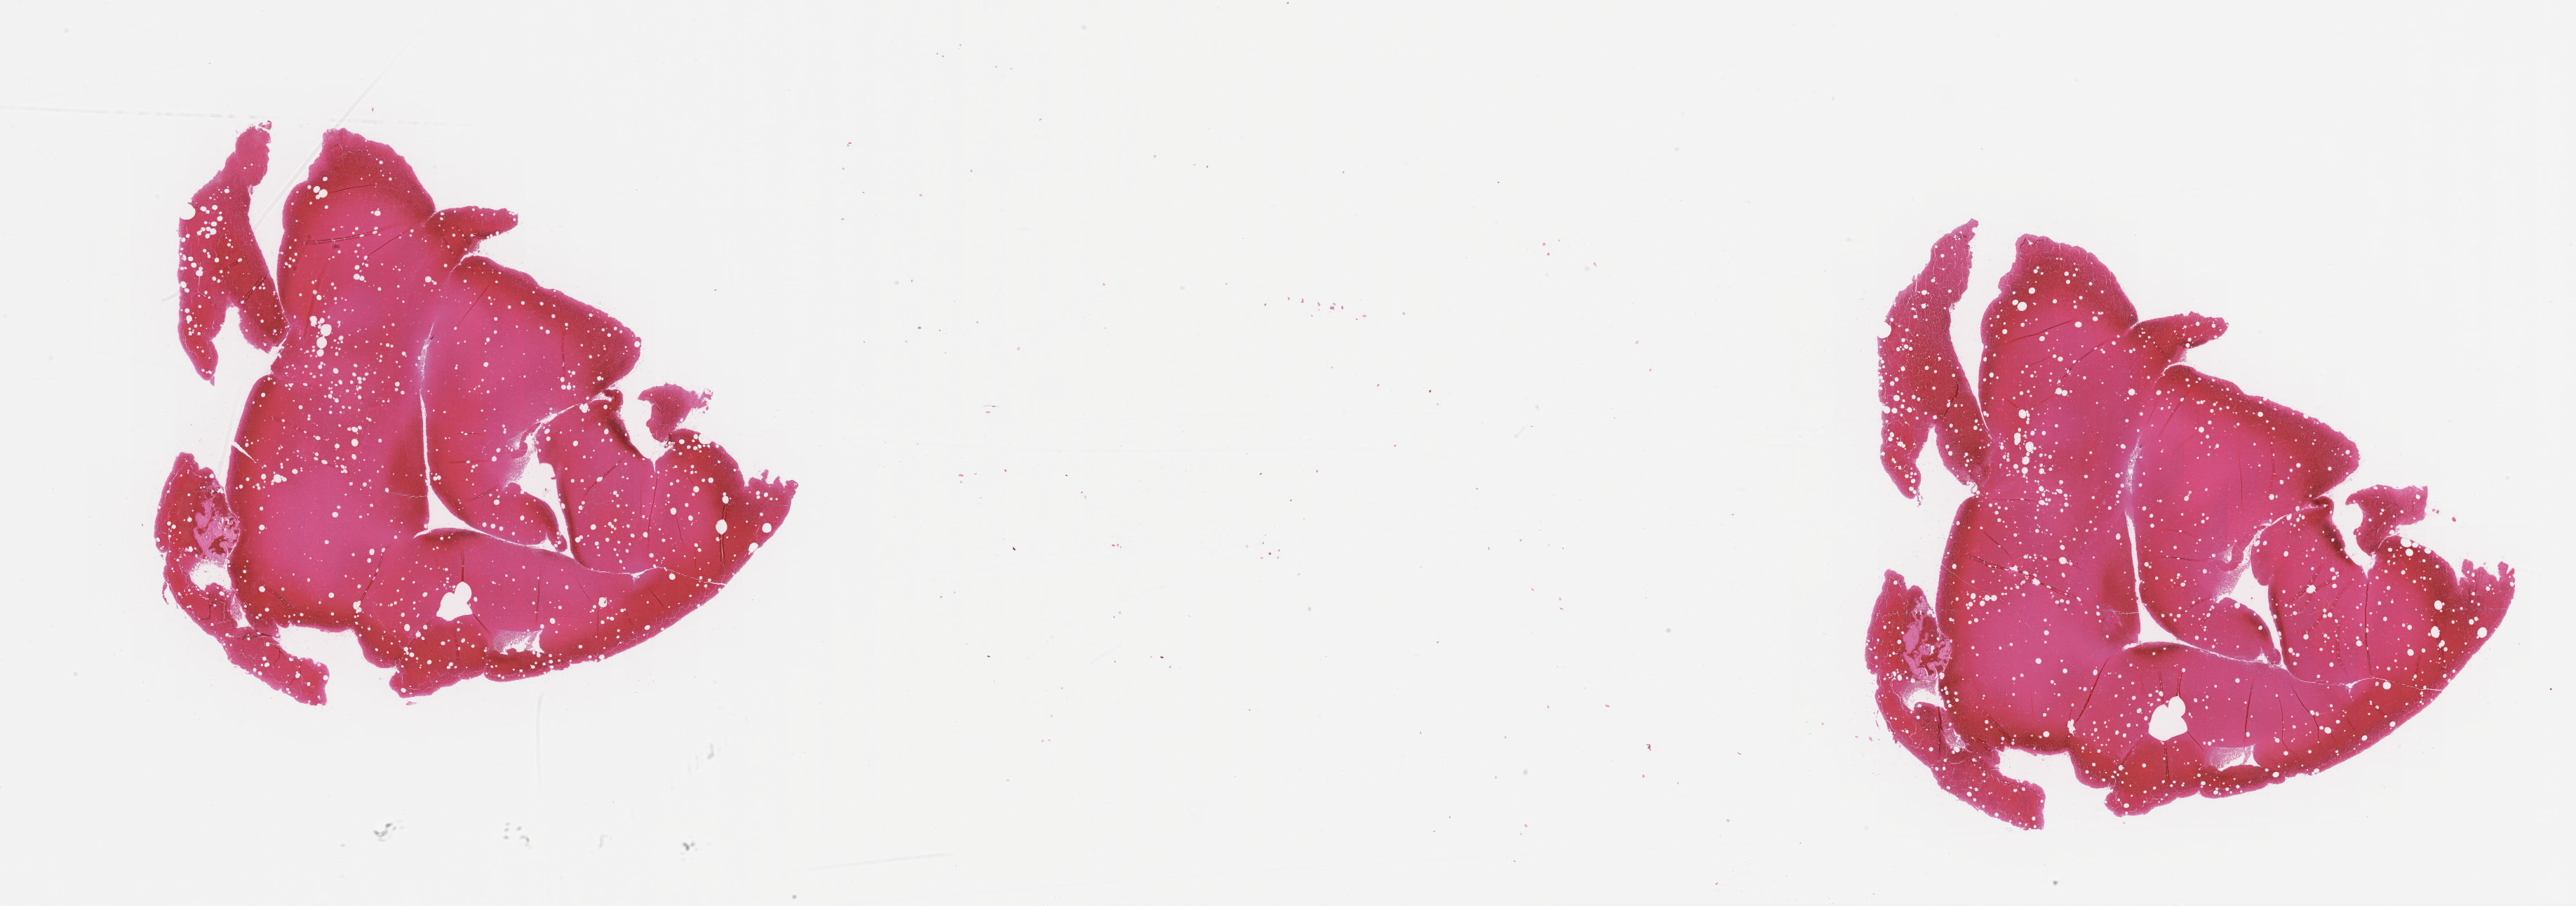
Digitized haematoxylin and eosin-stained section, shown as a low-resolution overview of the whole scanned area (about 29.7 x 10.4 mm). FFPE section. Tissue site: bone marrow. Specimen time point: archival tissue. Patient sex: female.
This section: primary tumor. Diagnosis: Plasma Cell Myeloma.